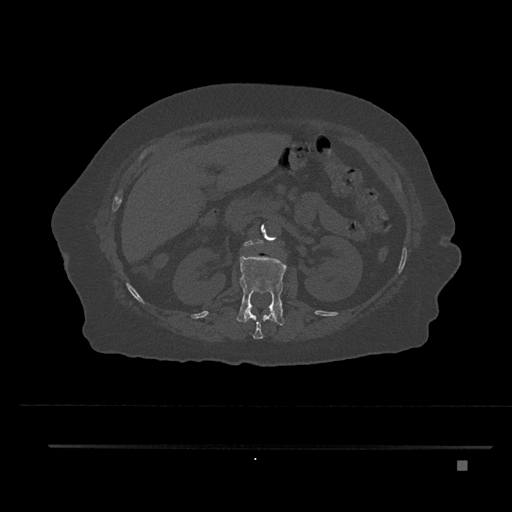
CT including the spine, one axial slice. Slice 228 of 797 in the series (ordered by position). Bone window (W 1800 / L 400 HU). 512 × 512 image matrix, field of view 437 × 437 mm. Female patient, age 76 years. Case-level facts recorded for this patient, not image findings: primary cancer: lung; vertebrae with lytic lesions (as recorded): T11, L3.
Annotated regions visible in this slice (semi-automatically segmented with operator editing):
- L1 vertebra: bounding box [x1, y1, x2, y2] px = [237, 254, 287, 326]
- L2 vertebra: [244, 239, 260, 247]
- T12 vertebra: [243, 307, 277, 339]